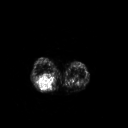
FDG PET of an extremity soft-tissue mass (from a PET/CT study), one axial slice; slice 171 of 267 in the series (ordered by position); 3.27 mm slice thickness; 128 × 128 image matrix, field of view 500 × 500 mm. Female patient, age 62 years. From the clinical record (not read from this slice): histological type: liposarcoma; site of the primary tumour: right thigh.
Annotated regions visible in this slice (expert contour drawn on MRI and transferred to this co-registered scan by the dataset authors):
- gross tumour volume (mass): bounding box (x1, y1, x2, y2) in pixels: (37, 75, 55, 91)